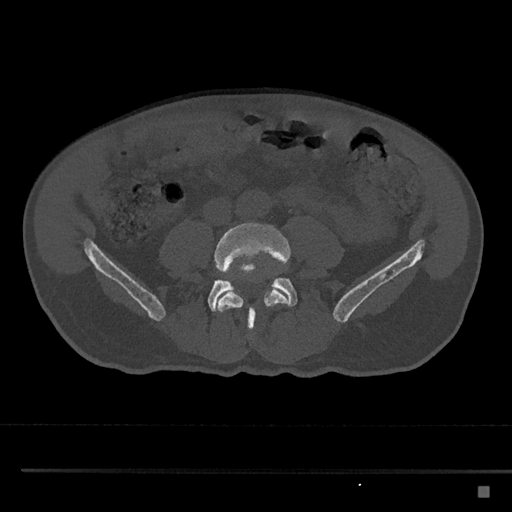
CT including the spine, one axial slice. Position 611 of 797 along the scan axis. Reconstruction kernel Br40s/3. 120 kVp. Bone window (W 1800 / L 400 HU). 0.5 mm slice thickness. 512 × 512 image matrix, field of view 391 × 391 mm. Patient: male, 59 years. From the clinical record (not read from this slice): primary cancer: prostate.
Structures marked on this image (semi-automatically segmented with operator editing):
- L4 vertebra: bounding box [x1, y1, x2, y2] px = [213, 222, 291, 332]
- L5 vertebra: [208, 271, 298, 312]